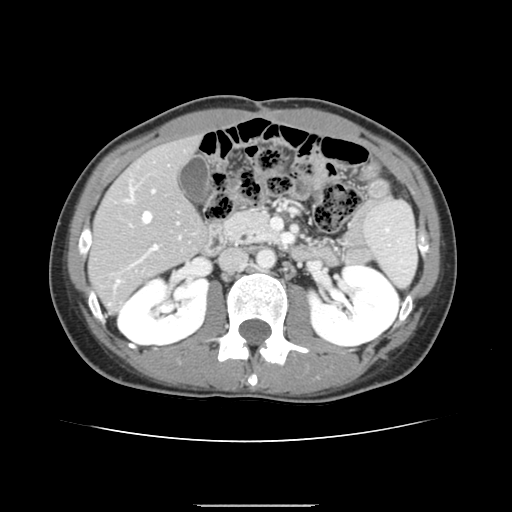
Contrast-enhanced abdominal CT, one axial slice; slice 70 of 150 in the series (ordered by position); intravenous contrast given; soft-tissue window (W 400 / L 40 HU); 512 × 512 image matrix, field of view 324 × 324 mm. Female patient, age 32 years. Case-level facts recorded for this patient, not image findings: diagnosis: colorectal cancer liver metastases, imaged before liver resection; multiple liver metastases: yes; largest metastasis: 0.7 cm; disease in both lobes: no.
Structures marked on this image (outlined manually by an expert reader):
- hepatic veins: bounding box [x1, y1, x2, y2] px = [117, 200, 152, 283]
- liver: [90, 139, 205, 309]
- planned liver remnant (the part of the liver to remain after resection): [90, 139, 205, 286]
- portal vein (with intrahepatic branches): [111, 184, 158, 305]